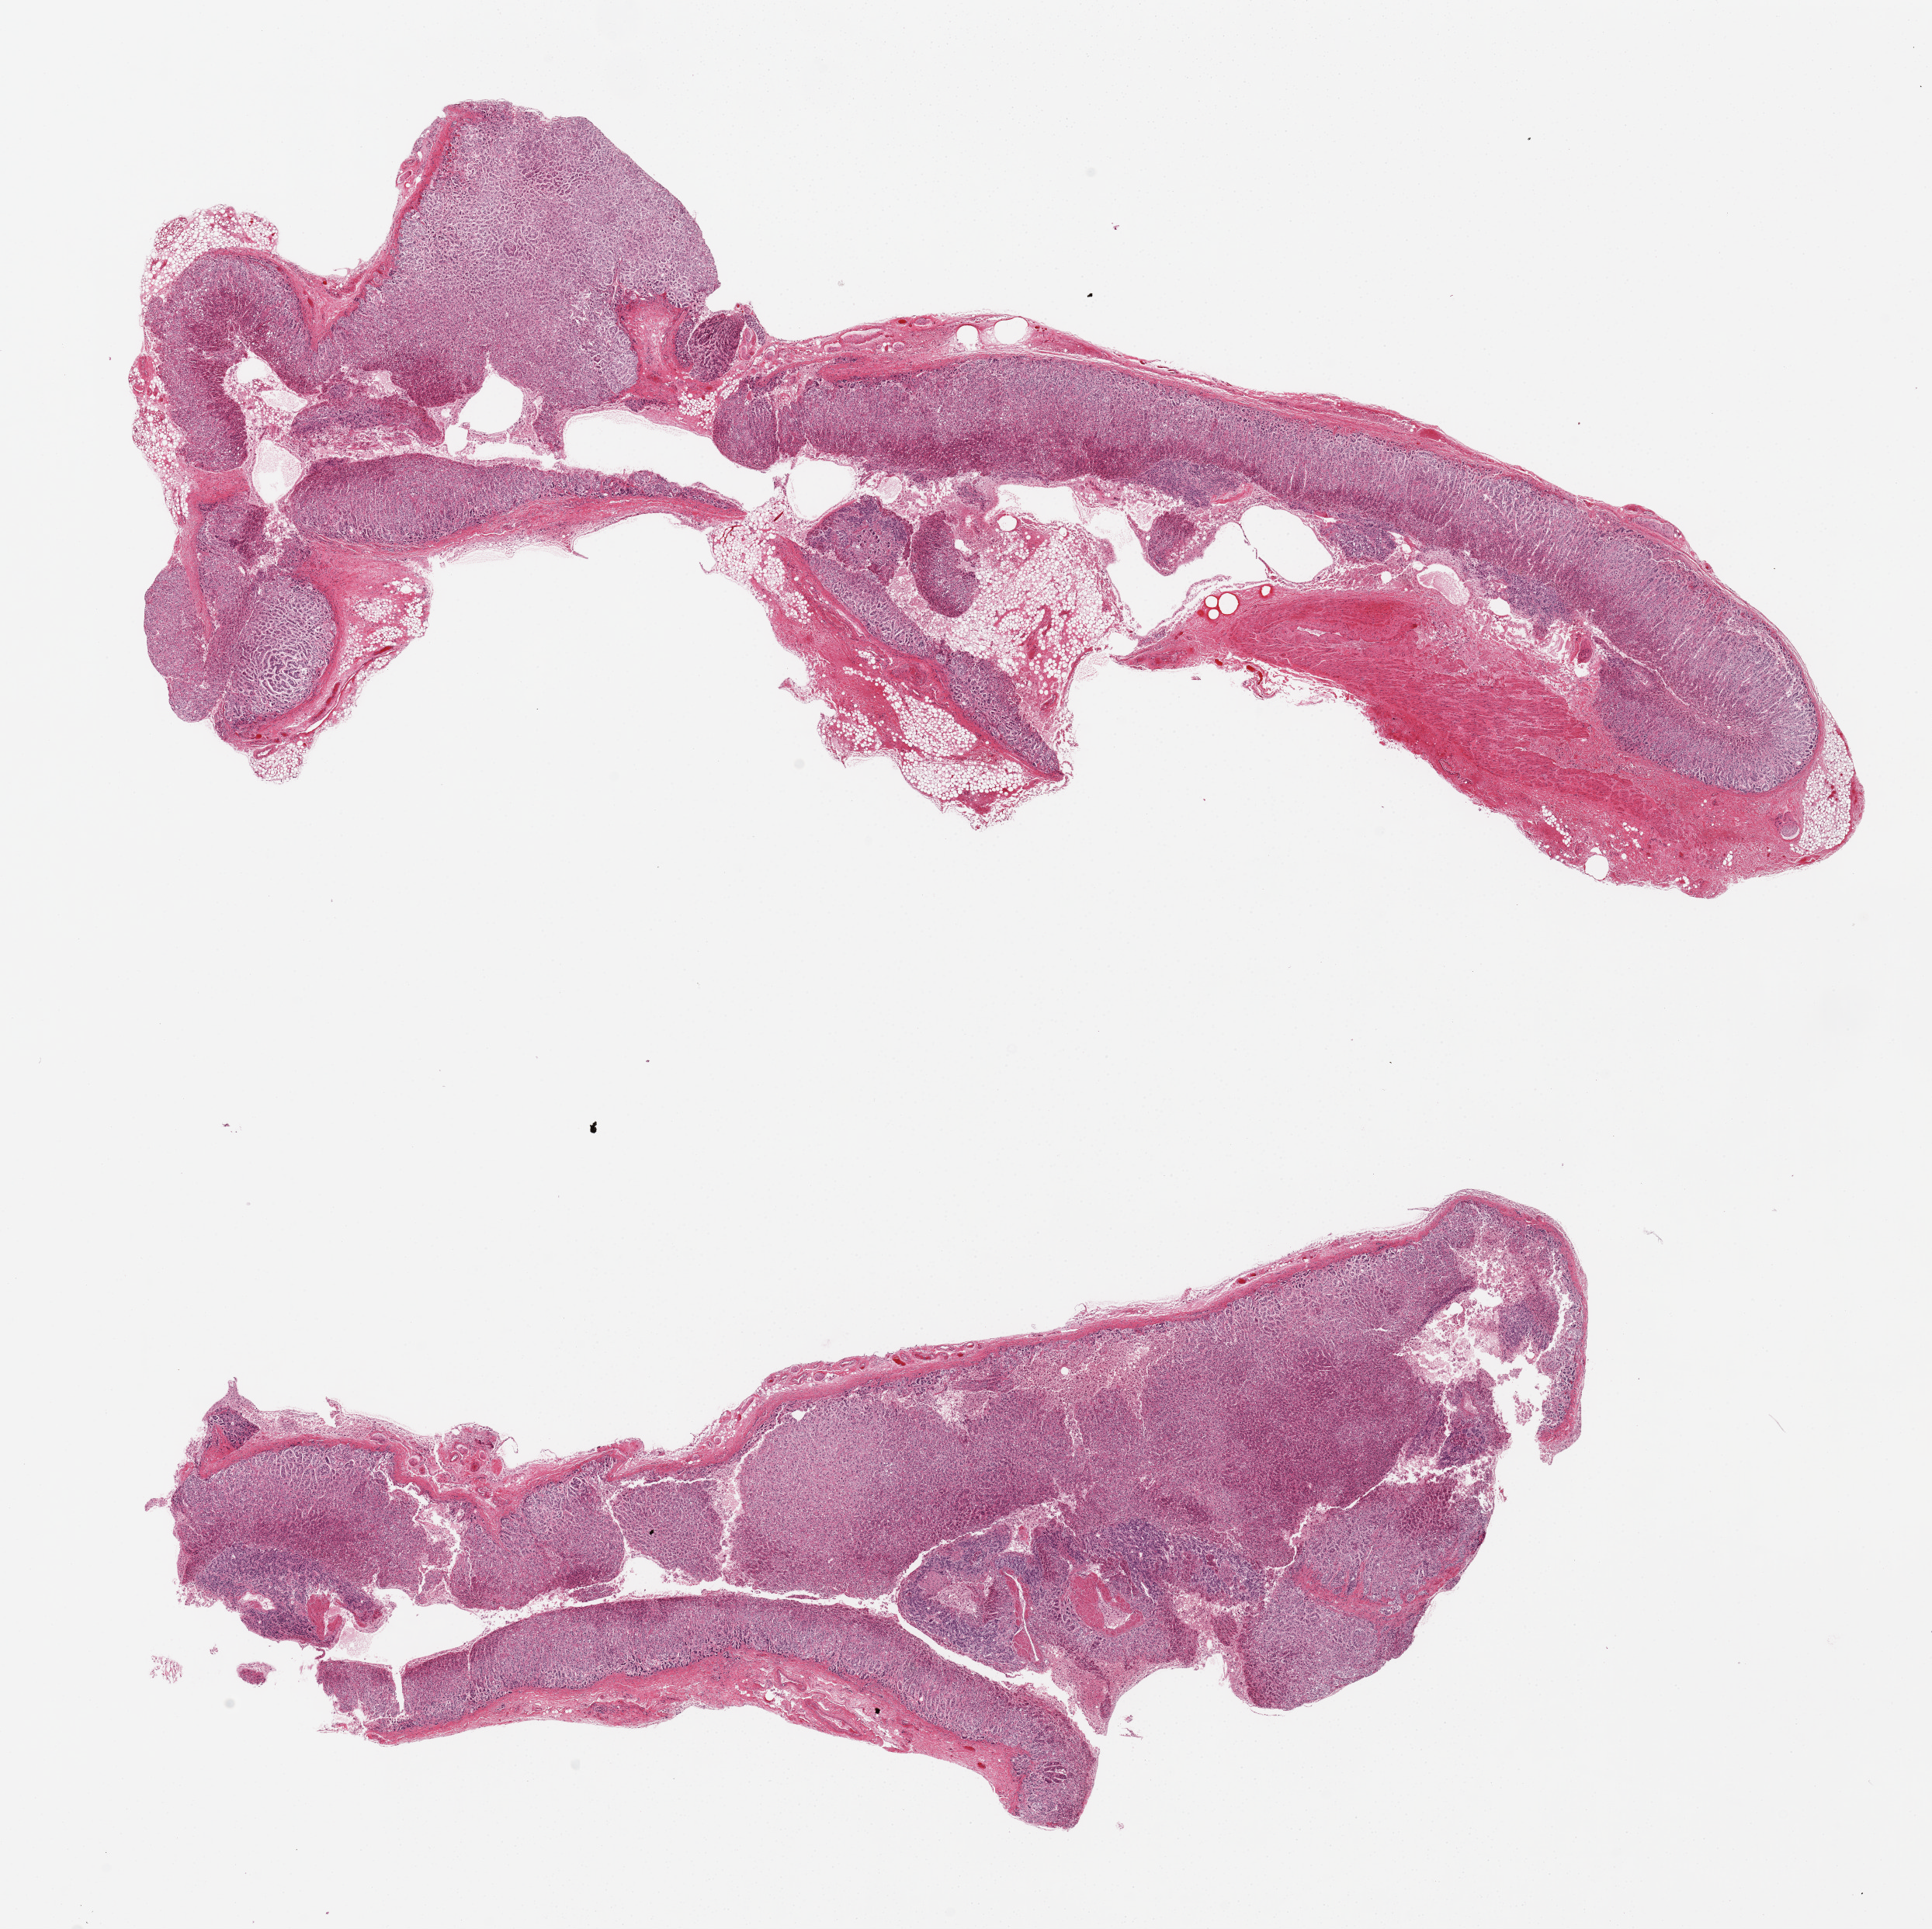
Whole-slide image, haematoxylin and eosin stain — whole scanned area (about 19.7 x 19.7 mm, from a 20x scan) shown as a low-resolution overview. PAXgene-fixed paraffin-embedded (PFPE) section. Sampled site (target tissue): adrenal gland. Donor tissue sample. Donor: female.
Pathologist's review note for this sample: 2 pieces, all cortex, one ~30% adherent/intermingled fat and fibroconnective tissue.